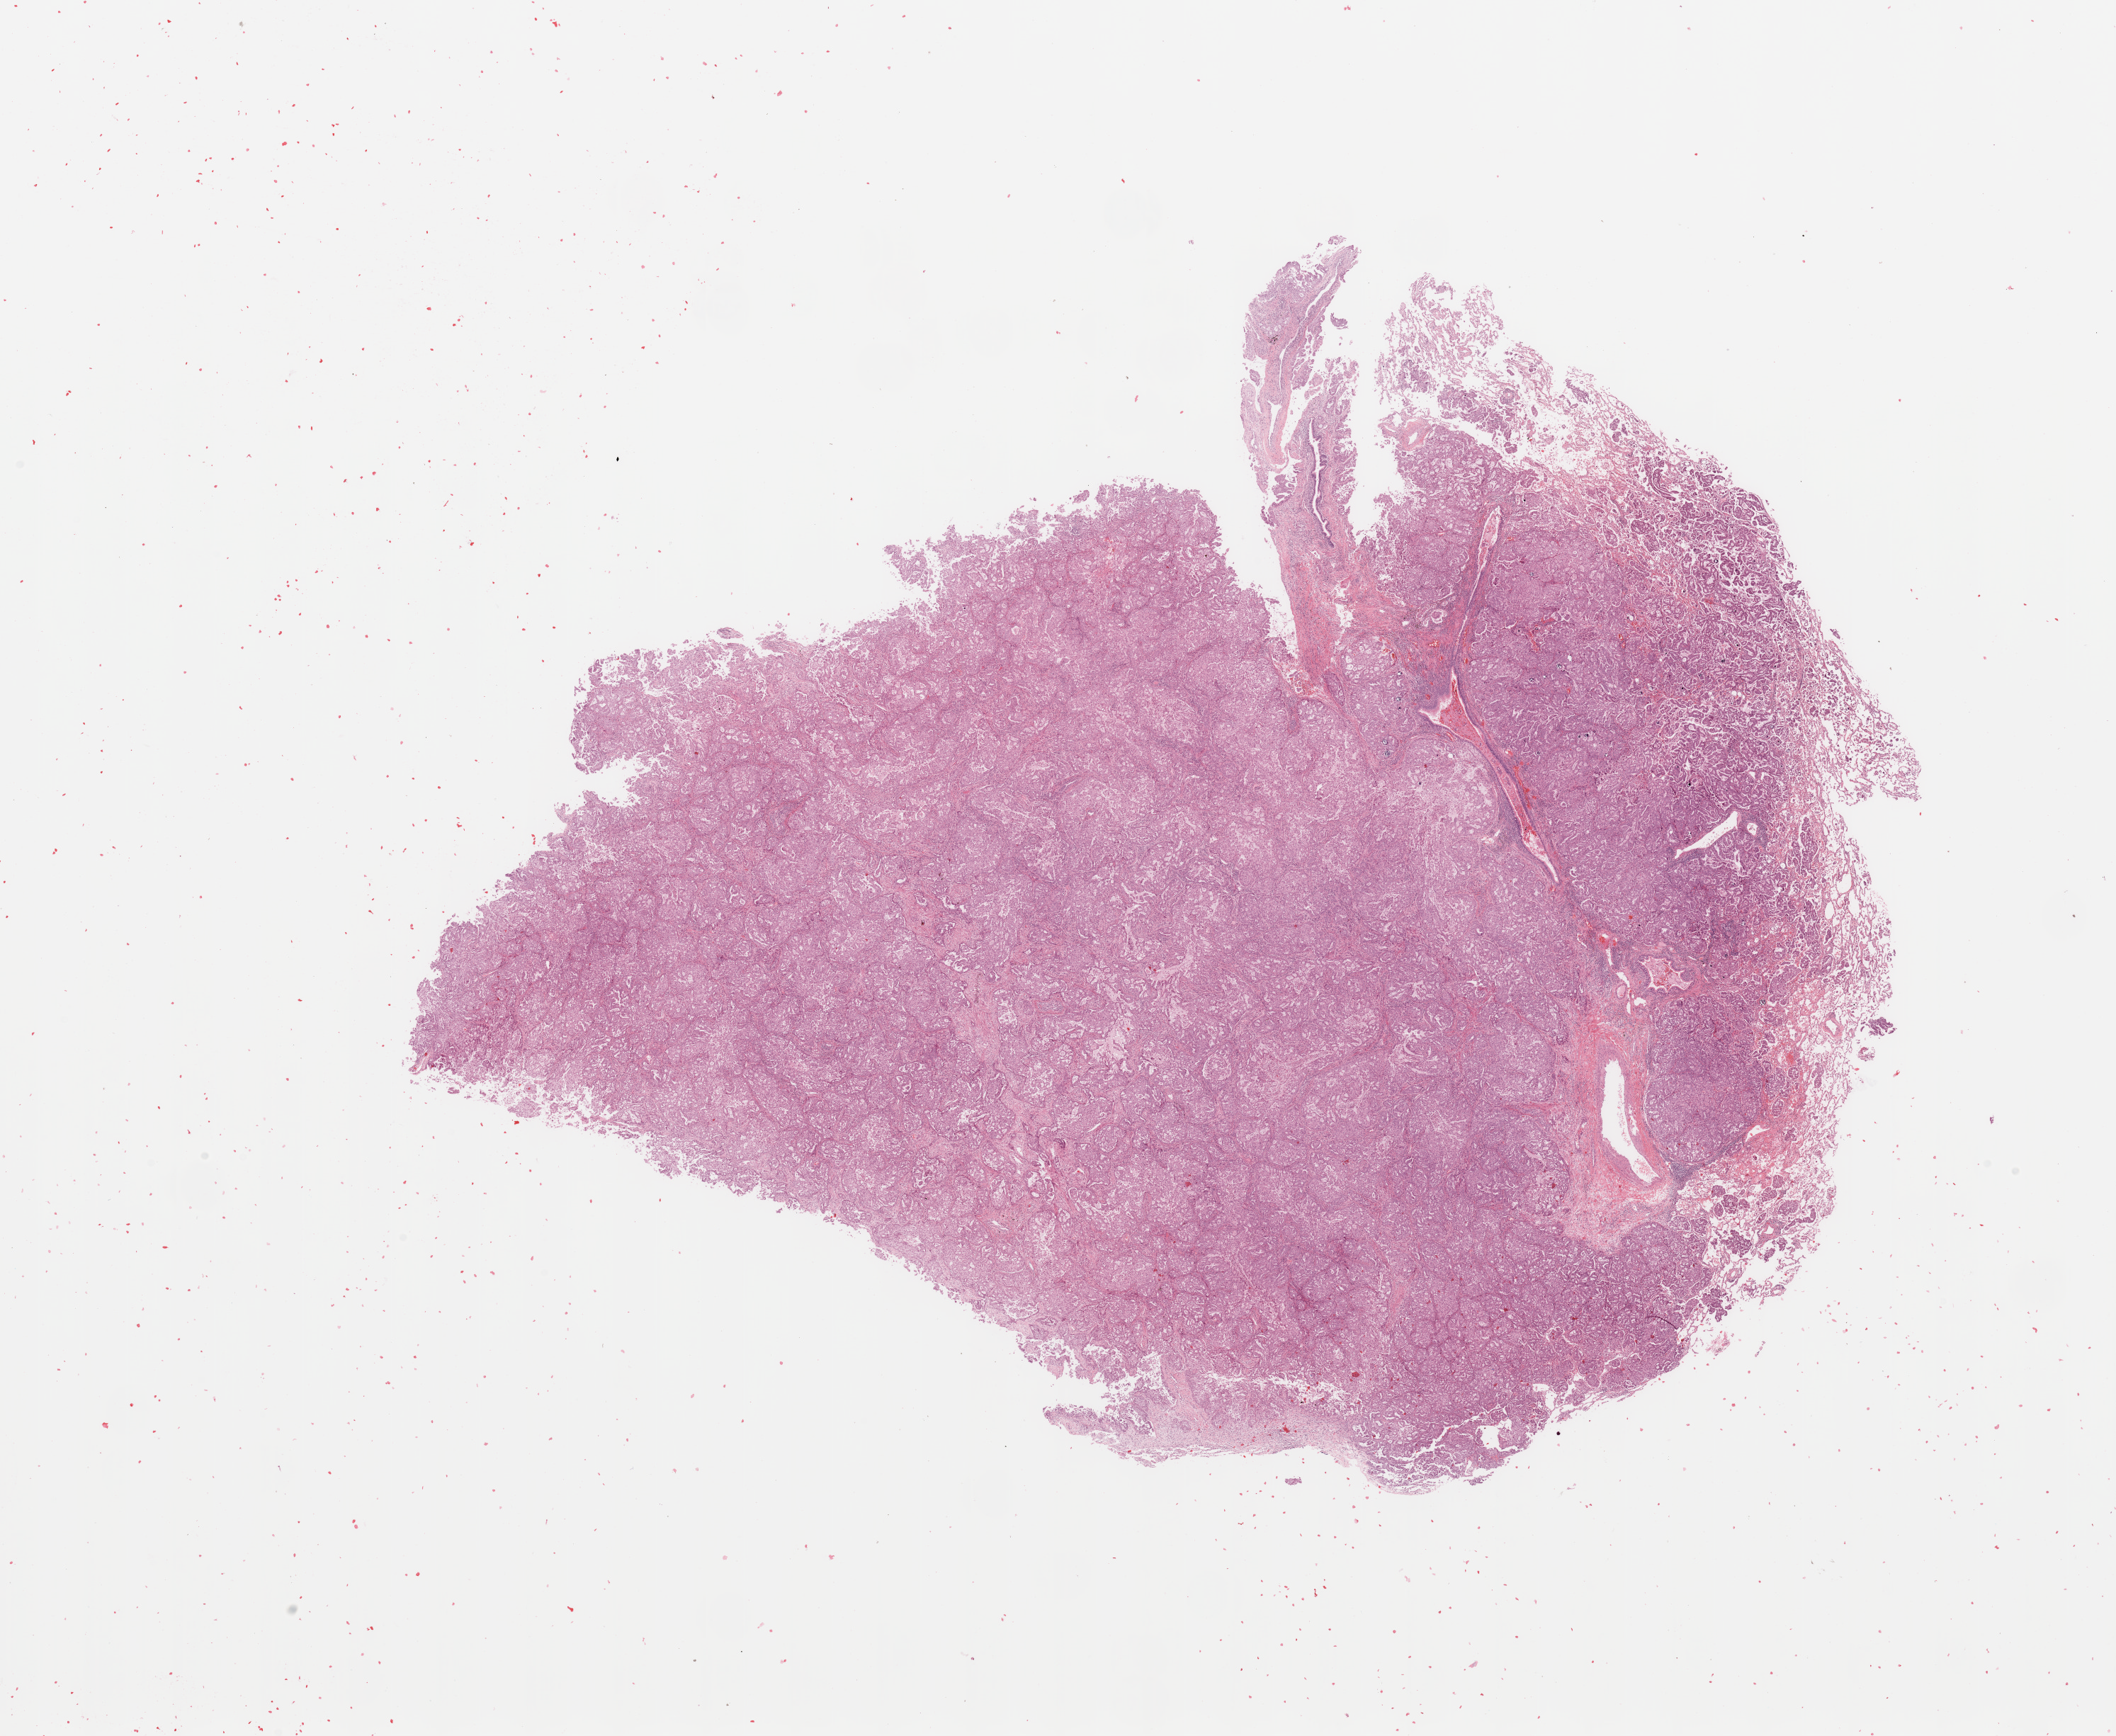
Digitized H&E-stained tissue section (whole slide), a low-resolution overview of the entire scanned area, about 23.6 x 19.4 mm (from a 20x scan). Lung, tumour tissue. Male, 58 y/o.
Diagnosis: Adenocarcinoma, NOS.